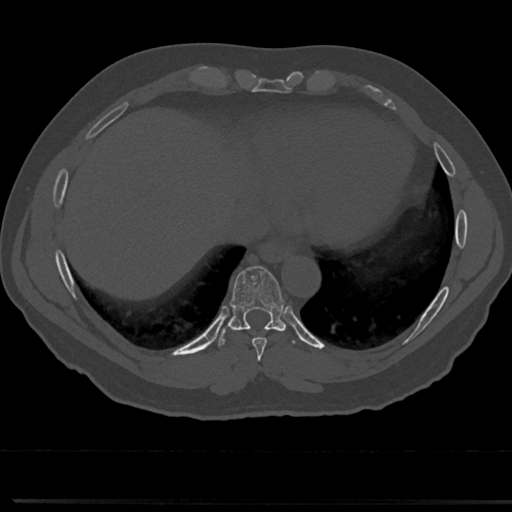
CT including the spine, one axial slice. Slice 322 of 817 in the series (ordered by position). Reconstruction kernel Br40s/3. 120 kVp. Bone window (W 1800 / L 400 HU). 512 × 512 image matrix, field of view 355 × 355 mm. Patient: male, 61 years. Case-level facts recorded for this patient, not image findings: primary cancer: prostate.
Outlined on this slice (semi-automatic segmentation, software-assisted and operator-edited):
- T7 vertebra: bounding box (x1, y1, x2, y2) in pixels: (258, 359, 266, 376)
- T8 vertebra: (214, 269, 308, 357)